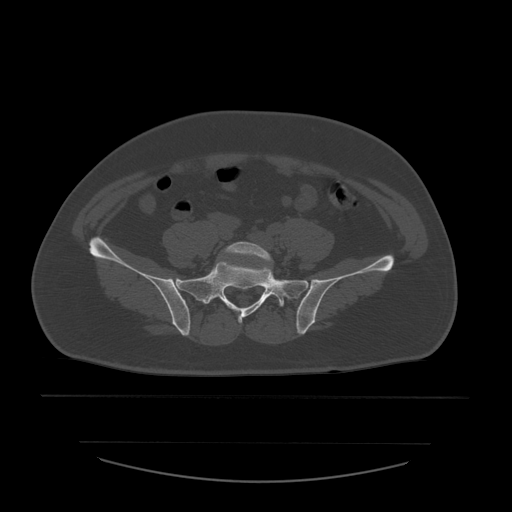
CT including the spine, one axial slice; position 104 of 532 along the scan axis; reconstruction kernel STANDARD; 120 kVp; bone window (W 1800 / L 400 HU); 512 × 512 image matrix, field of view 441 × 441 mm. Patient age 44 years. From the clinical record (not read from this slice): primary cancer: soft tissue sarcoma.
Outlined on this slice (semi-automatic segmentation, software-assisted and operator-edited):
- L5 vertebra: bounding box [x1, y1, x2, y2] px = [224, 242, 281, 307]